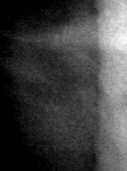
Cropped region of a digitized screen-film mammogram centred on a radiologist-marked abnormality, right breast, MLO view, BI-RADS breast density category 3 (scale 1–4).
Marked abnormality: mass, shape architectural distortion; BI-RADS assessment category 2; subtlety rating 3 on a 1 (subtle) to 5 (obvious) scale; pathology result (as recorded, not read from the image): benign.